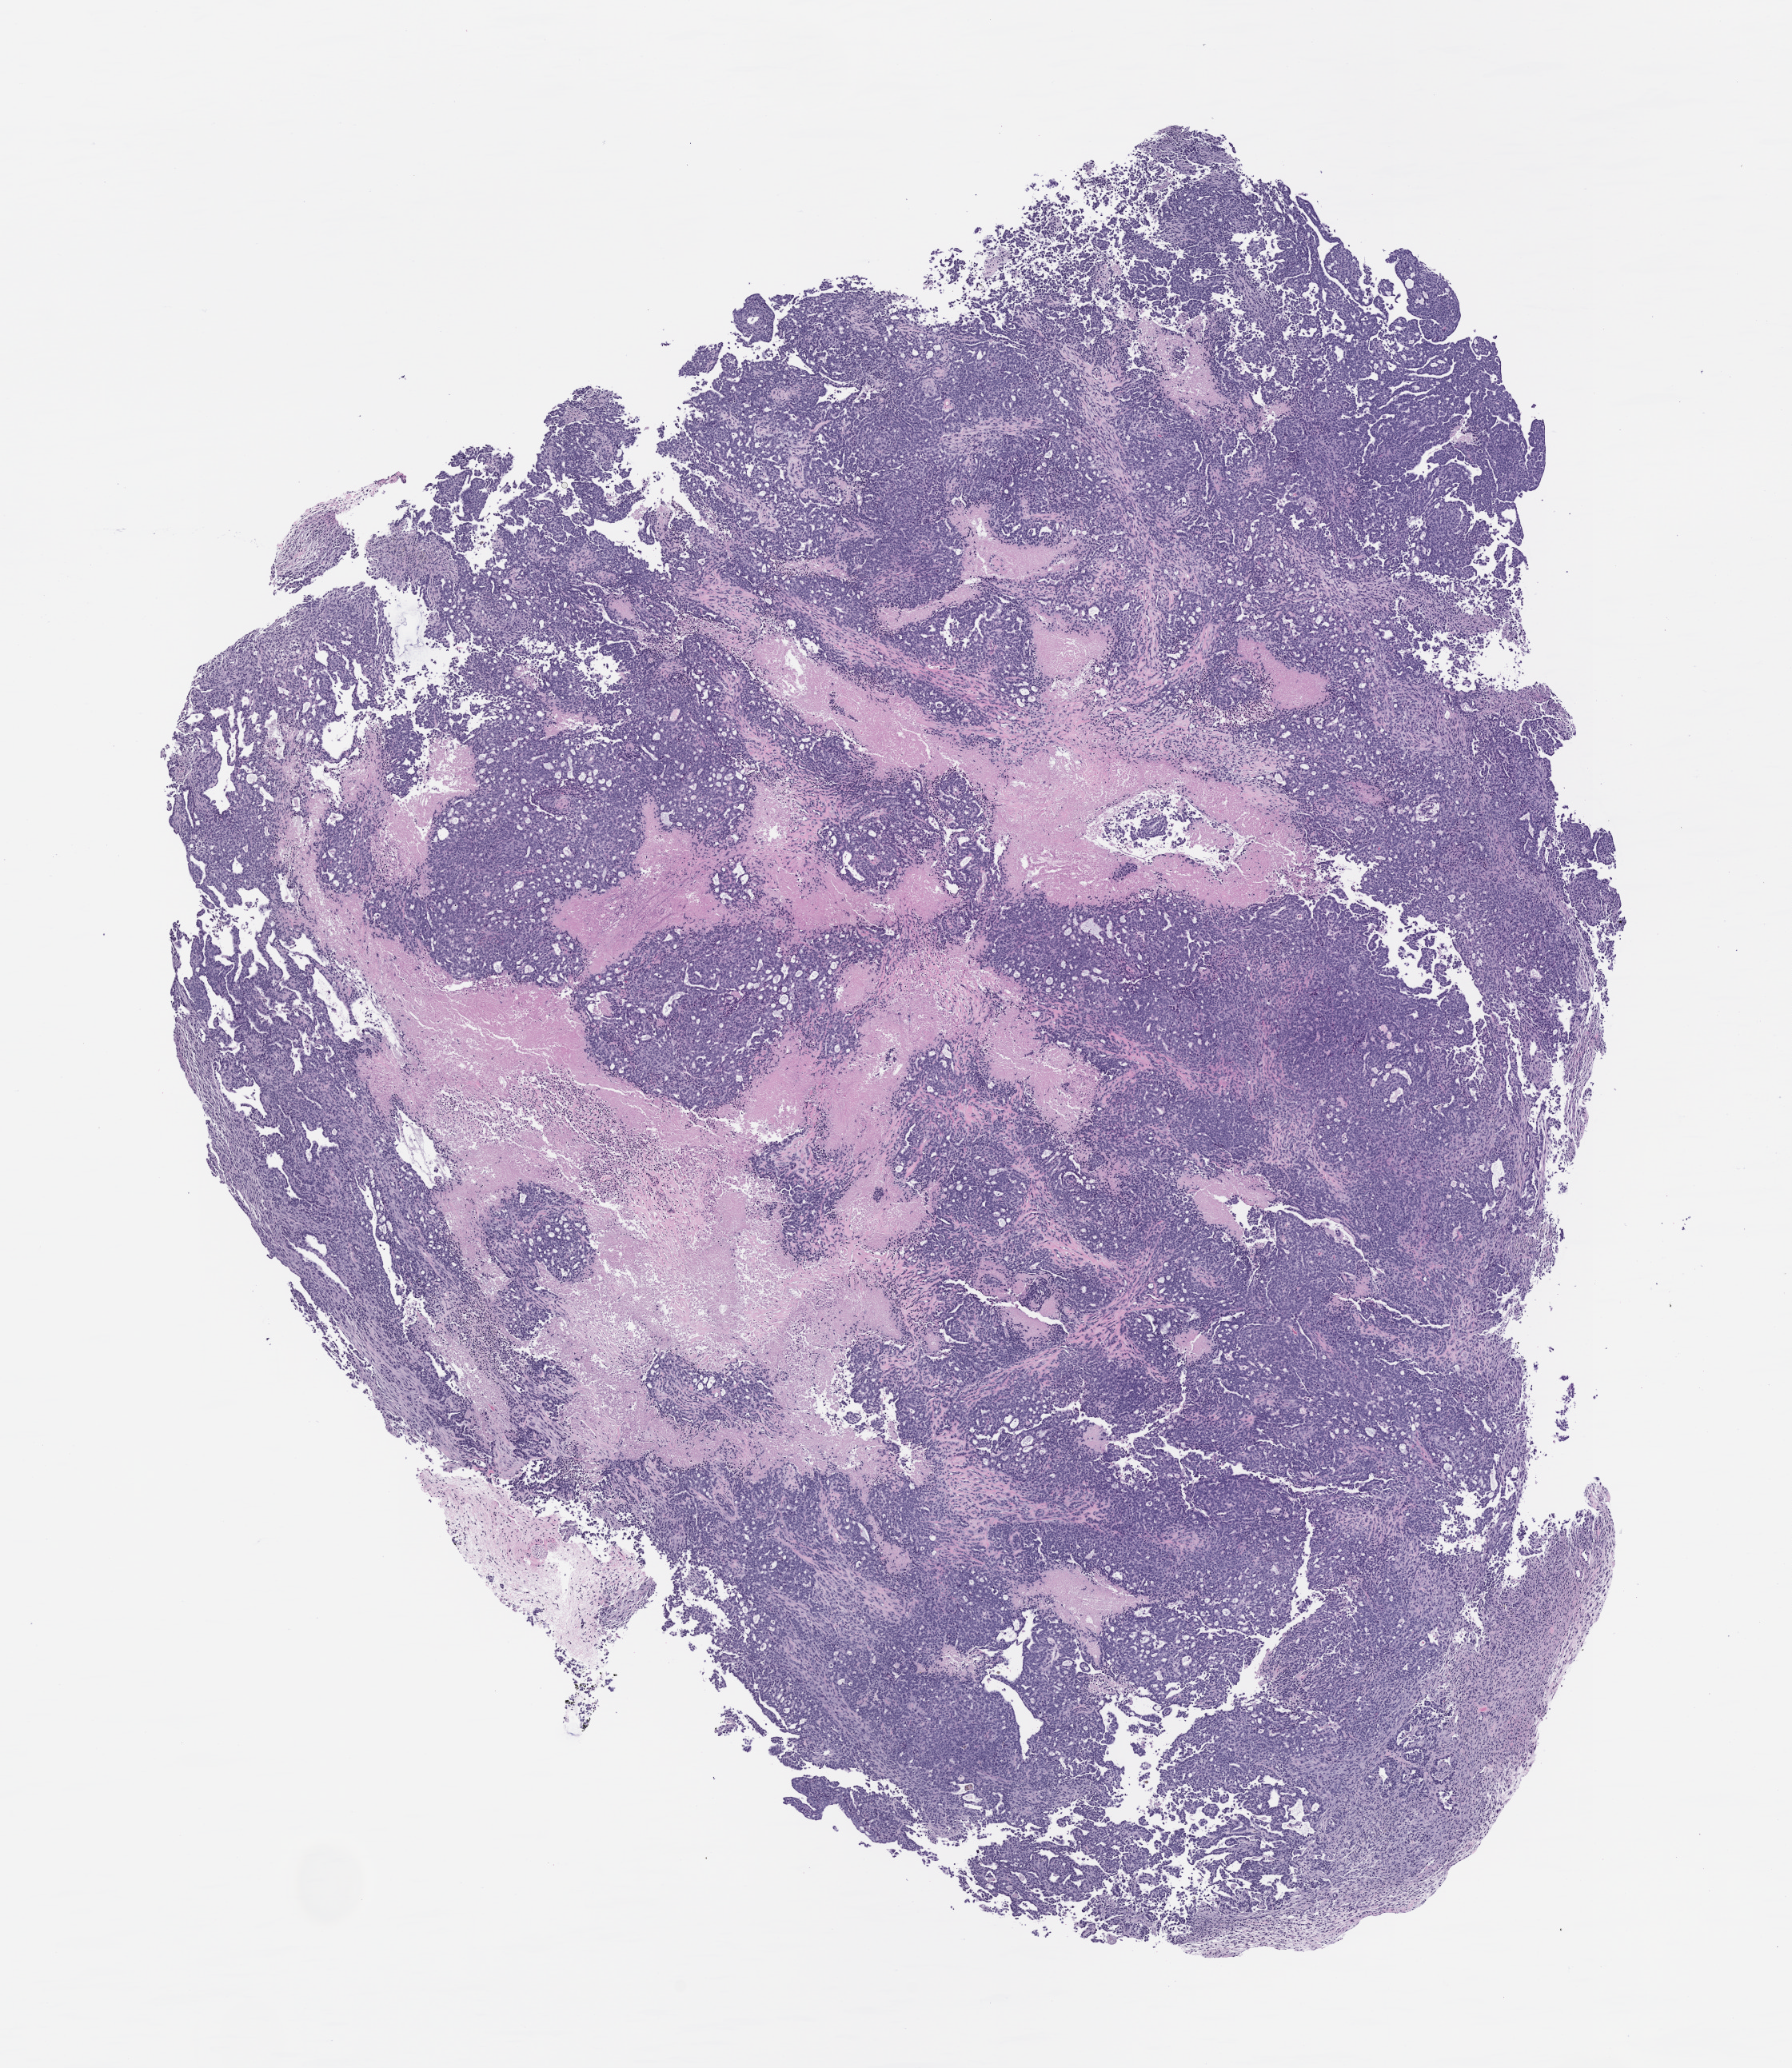
Whole-slide image, haematoxylin and eosin: patient-derived xenograft (human tumor grown in a mouse), passage 1 — a low-resolution overview of the entire scanned area, about 9.0 x 10.4 mm; FFPE section.
Originating patient diagnosis: Mesothelial Neoplasm.